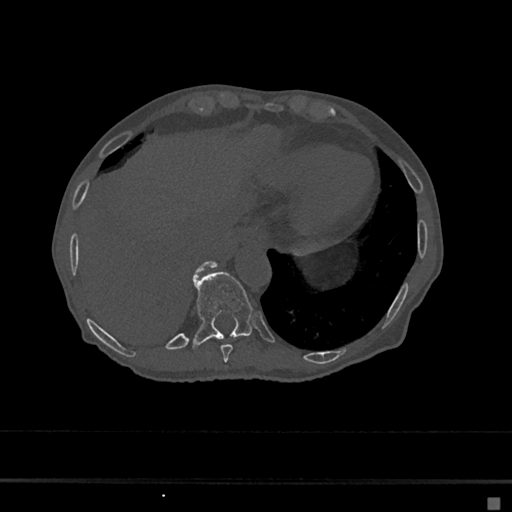
CT including the spine, one axial slice. Reconstruction kernel Br40s/3. Bone window (W 1800 / L 400 HU). 0.5 mm slice thickness. 512 × 512 image matrix. Patient: female, 68 years. From the clinical record (not read from this slice): primary cancer: renal.
Outlined on this slice (semi-automatically segmented with operator editing):
- T10 vertebra: box from (x=193, y=271) to (x=256, y=346) px
- T11 vertebra: (x=195, y=261)–(x=217, y=276)
- T9 vertebra: (x=220, y=344)–(x=233, y=363)